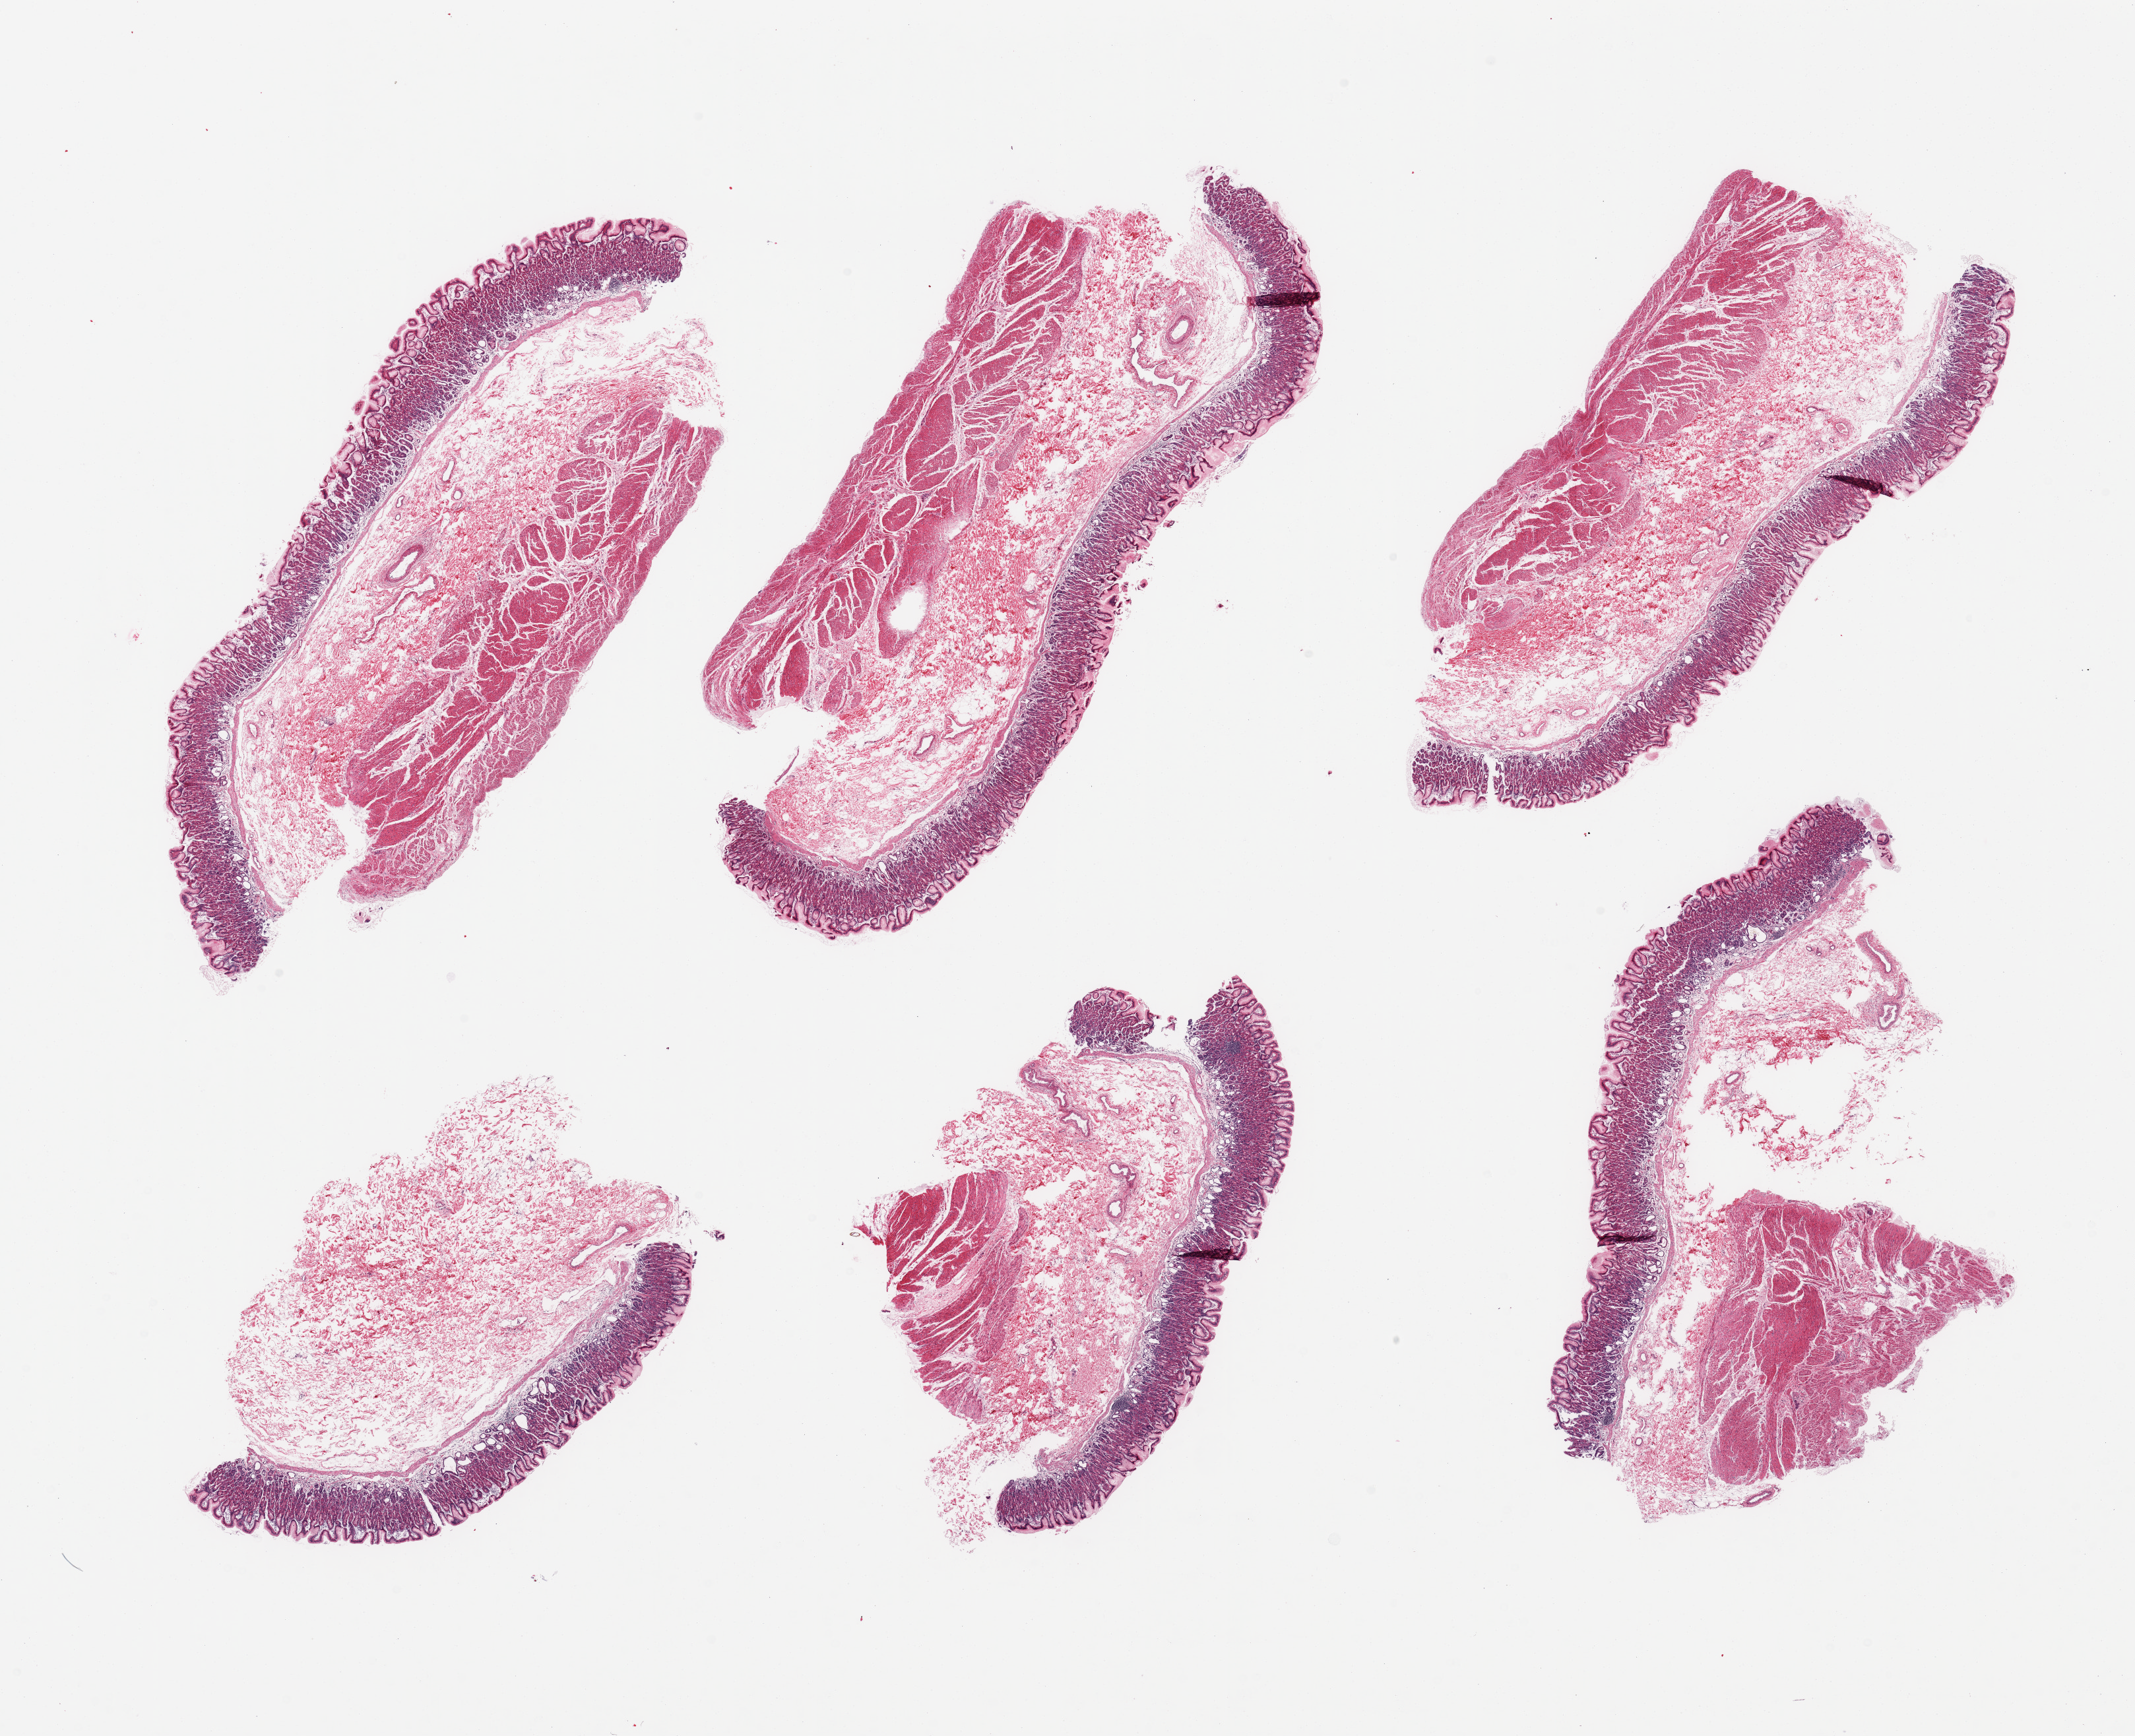
Whole-slide image, hematoxylin and eosin (H&E) stain, a low-resolution overview of the entire scanned area, about 25.6 x 20.8 mm (acquisition: 20x scan). PAXgene-fixed, paraffin-embedded tissue. Target tissue: stomach. Tissue donor sample. Male donor.
- pathologist's review note for this sample: 6 pieces; 5 are full thickness, 1 is mucosa/submucosa, basal glandular dilatation